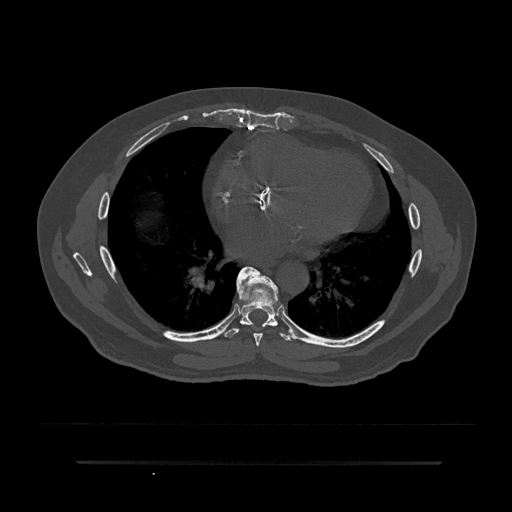
CT including the spine, one axial slice. Slice 451 of 797 in the series (ordered by position). Reconstruction kernel Br40s/3. 120 kVp. Bone window (W 1800 / L 400 HU). 512 × 512 image matrix, field of view 464 × 464 mm. Male patient, age 59 years. Case-level facts recorded for this patient, not image findings: primary cancer: bile ducts; vertebrae with lytic lesions (as recorded): T10.
Outlined on this slice (semi-automatic segmentation, software-assisted and operator-edited):
- T7 vertebra: box from (x=236, y=266) to (x=266, y=346) px
- T8 vertebra: (x=223, y=269)–(x=295, y=341)